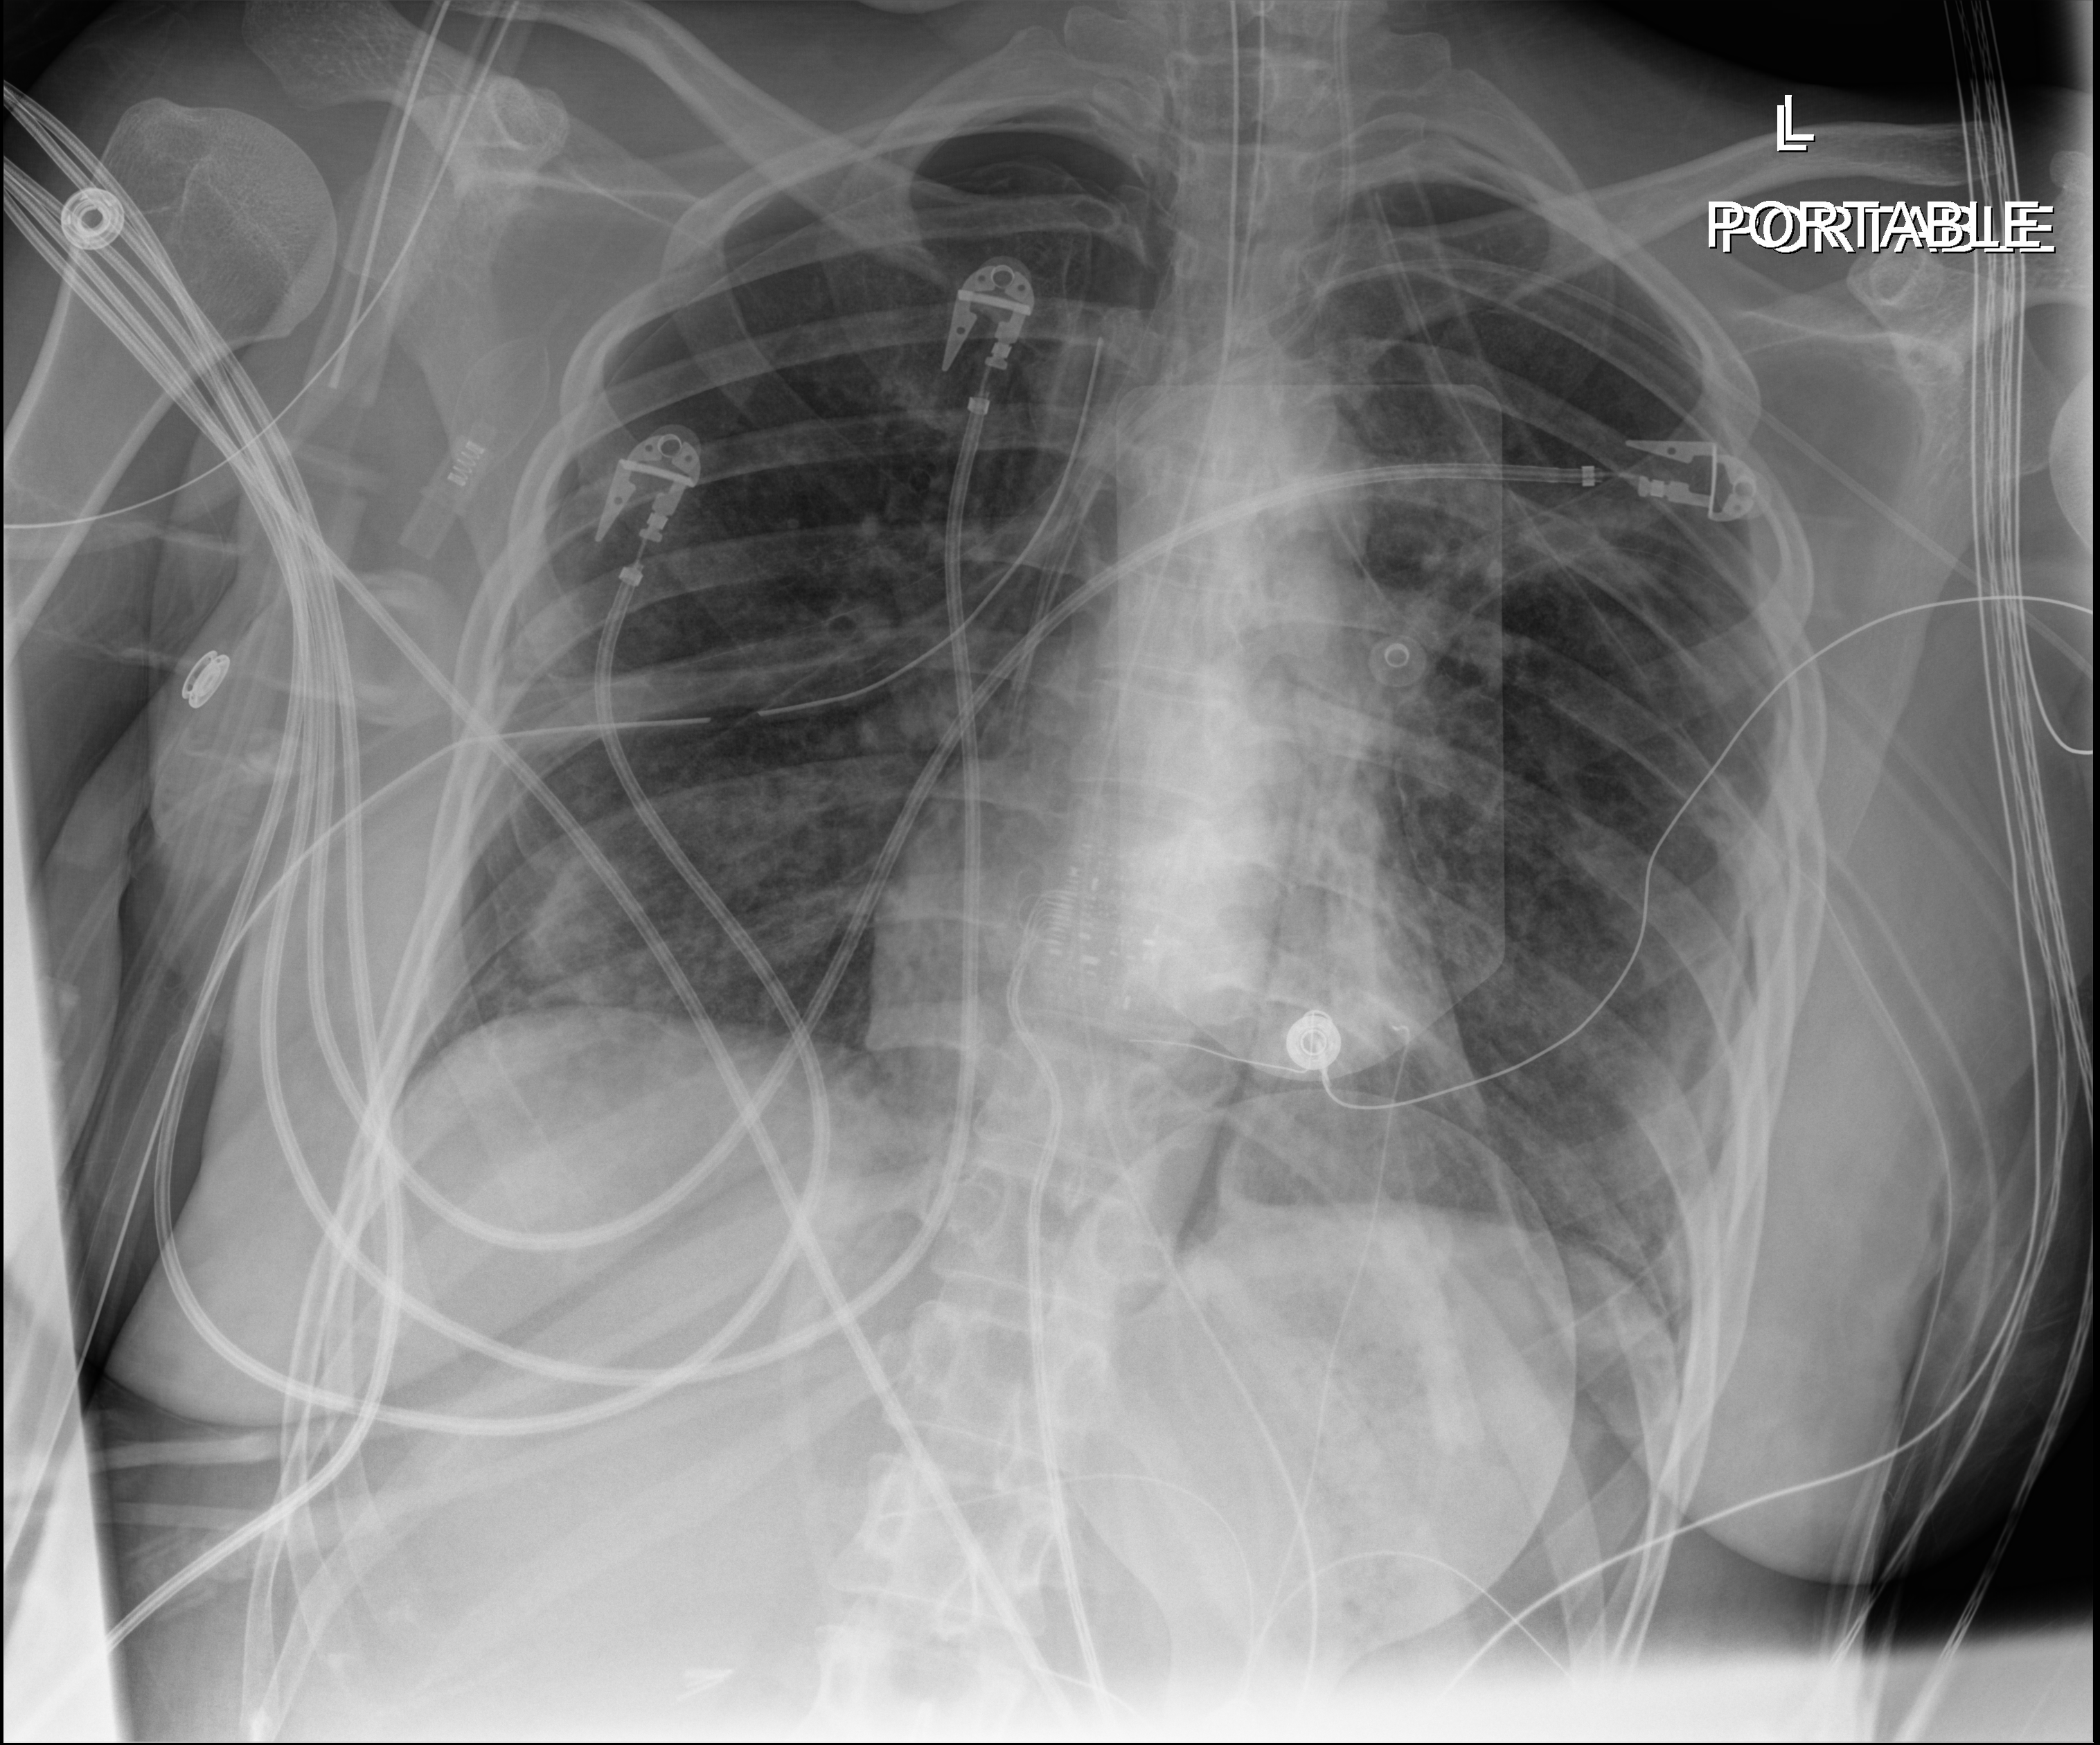
Bedside chest radiograph (digital radiography); anteroposterior (AP) projection. Patient hospitalised with COVID-19, aged 18–59 years.
From the hospital-stay record, not from the radiograph (when in the stay this image was taken is not recorded): admitted to intensive care during this hospital stay: yes; mechanically ventilated during this hospital stay: yes; hypertension (admission record): no.